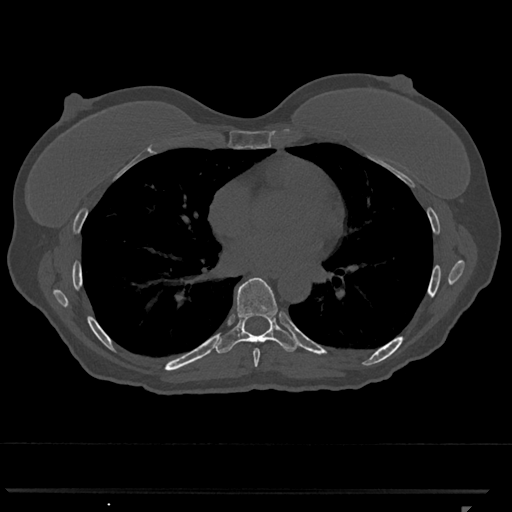
CT including the spine, one axial slice. Slice 676 of 793 in the series (ordered by position). Reconstruction kernel Br40s/3. 120 kVp. Bone window (W 1800 / L 400 HU). 0.5 mm slice thickness. 512 × 512 image matrix, field of view 380 × 380 mm. Patient: female, 62 years. Case-level facts recorded for this patient, not image findings: primary cancer: renal.
Annotated regions visible in this slice (semi-automatic segmentation, software-assisted and operator-edited):
- T7 vertebra: bounding box [x1, y1, x2, y2] px = [253, 349, 260, 367]
- T8 vertebra: [214, 277, 298, 354]